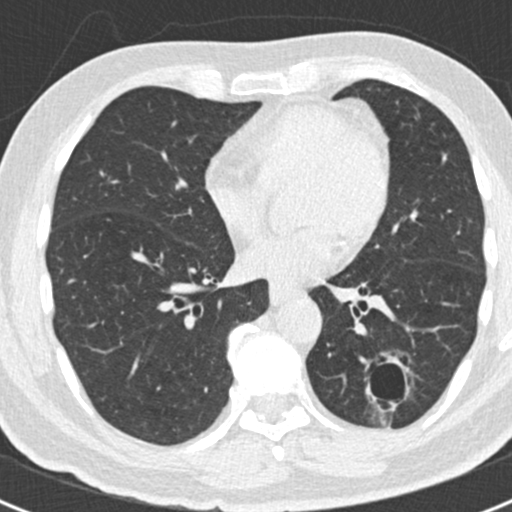
Low-dose screening chest CT, axial slice, baseline annual screen, lung window (W 1500 / L -600 HU), 2 mm slice thickness, standard (soft-tissue) reconstruction kernel (B30f), slice 97 of 188 in the series, 512 × 512 image matrix, field of view 300 × 300 mm. Male, age 66 years at enrolment. Former smoker at enrolment.
• Expert-annotated lung lesion, bounding box (x1, y1, x2, y2) in pixels: (345, 340, 421, 419).
• Screening reader's record for this exam (one nodule recorded; not confirmed to be the boxed lesion): non-calcified nodule or mass ≥4 mm, left lower lobe, 43 × 27 mm, smooth margins.
• Participant outcome: lung cancer diagnosed 801 days after this screen (after the third annual screen) — adenocarcinoma, NOS, left lower lobe, poorly differentiated (G3), stage IB (AJCC 6th edition), 38 mm at pathology.